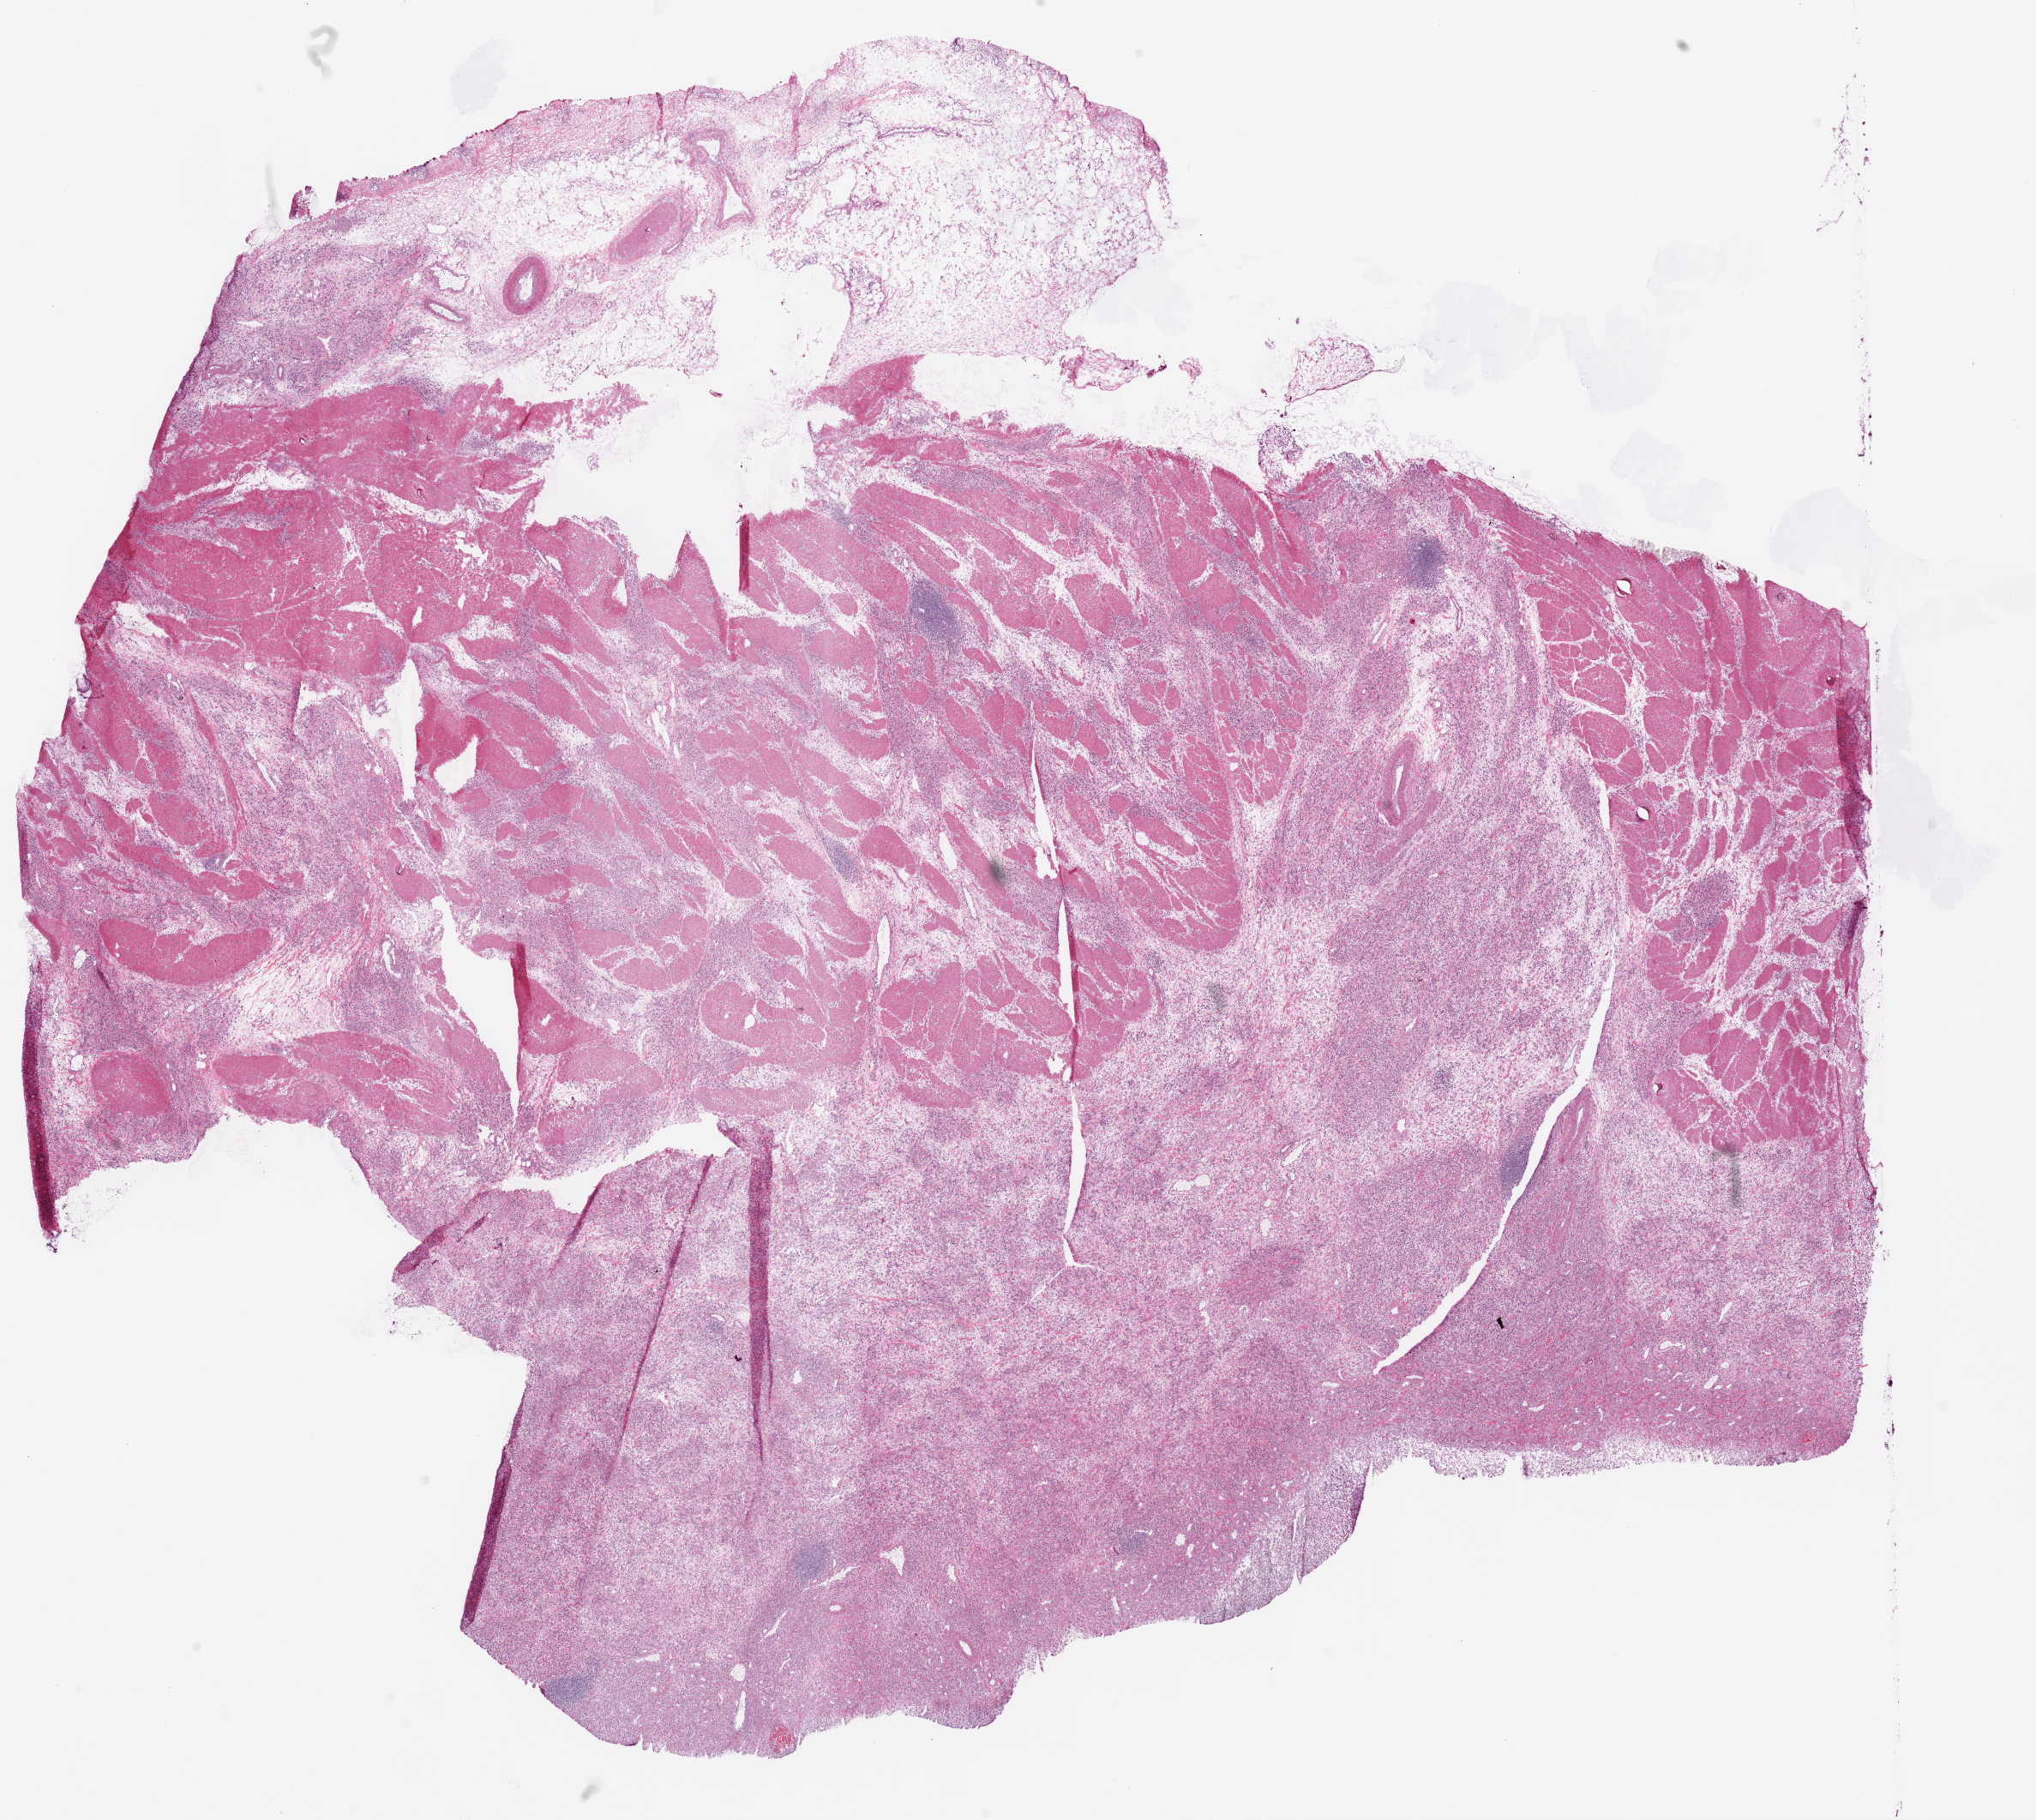
Digitized Hematoxylin and eosin (H&E) stained tissue section (whole slide), low-resolution overview of the scanned area, about 19.1 x 17.0 mm (from a 20x scan), frozen section from the top of the tissue portion, primary tumour sample from the stomach. Male, age 56 years at initial diagnosis. Histologic grade: G3 (poorly differentiated). Slide review estimates, as recorded: tumour cells 70%, tumour nuclei 85%, normal cells 15%, stromal cells 15%, necrosis 0%.
• pathologic diagnosis: Adenocarcinoma, NOS (gastric antrum)